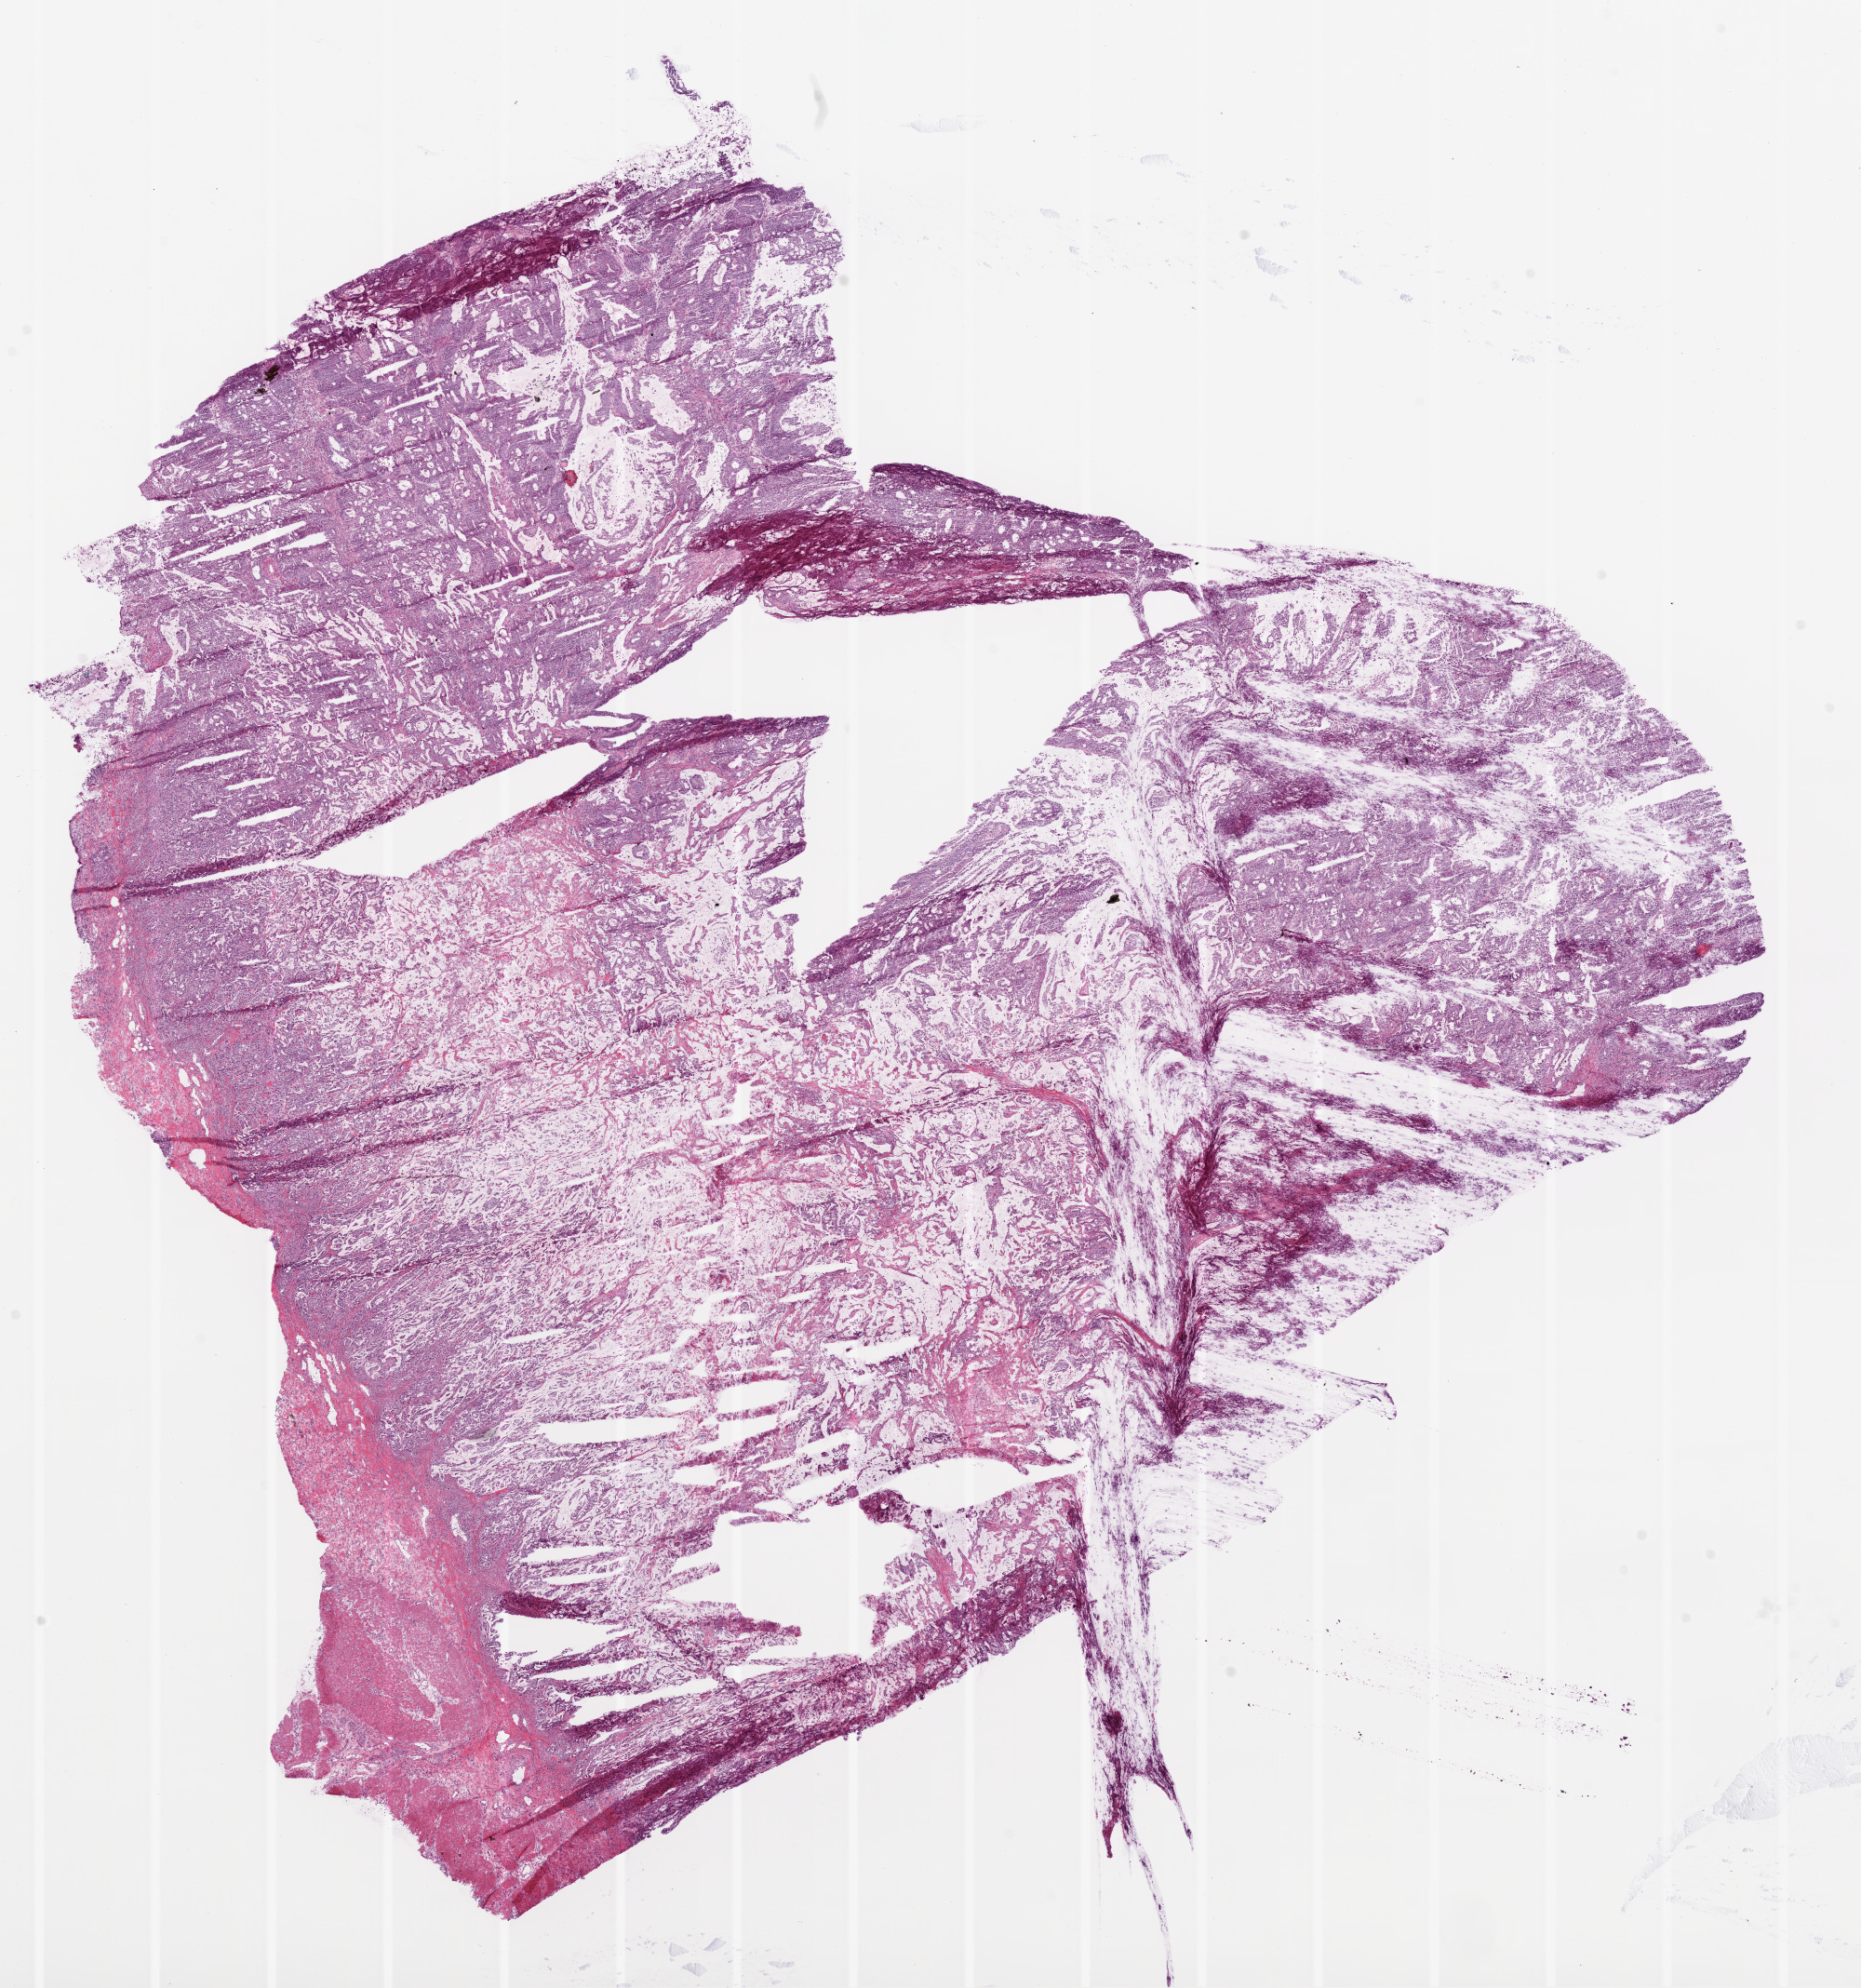
Digitized Hematoxylin and eosin (H&E) stained tissue section (whole slide) — low-resolution overview of the scanned area, about 16.0 x 17.1 mm; frozen section from the bottom of the tissue portion; sample: primary tumour, stomach. Female, age 79 years at initial diagnosis. Histologic grade: G2 (moderately differentiated). Composition of this section per pathologist review: tumour cells 82%, tumour nuclei 85%, normal cells 5%, stromal cells 10%, necrosis 3%.
Diagnosis: Adenocarcinoma, NOS (gastric antrum).